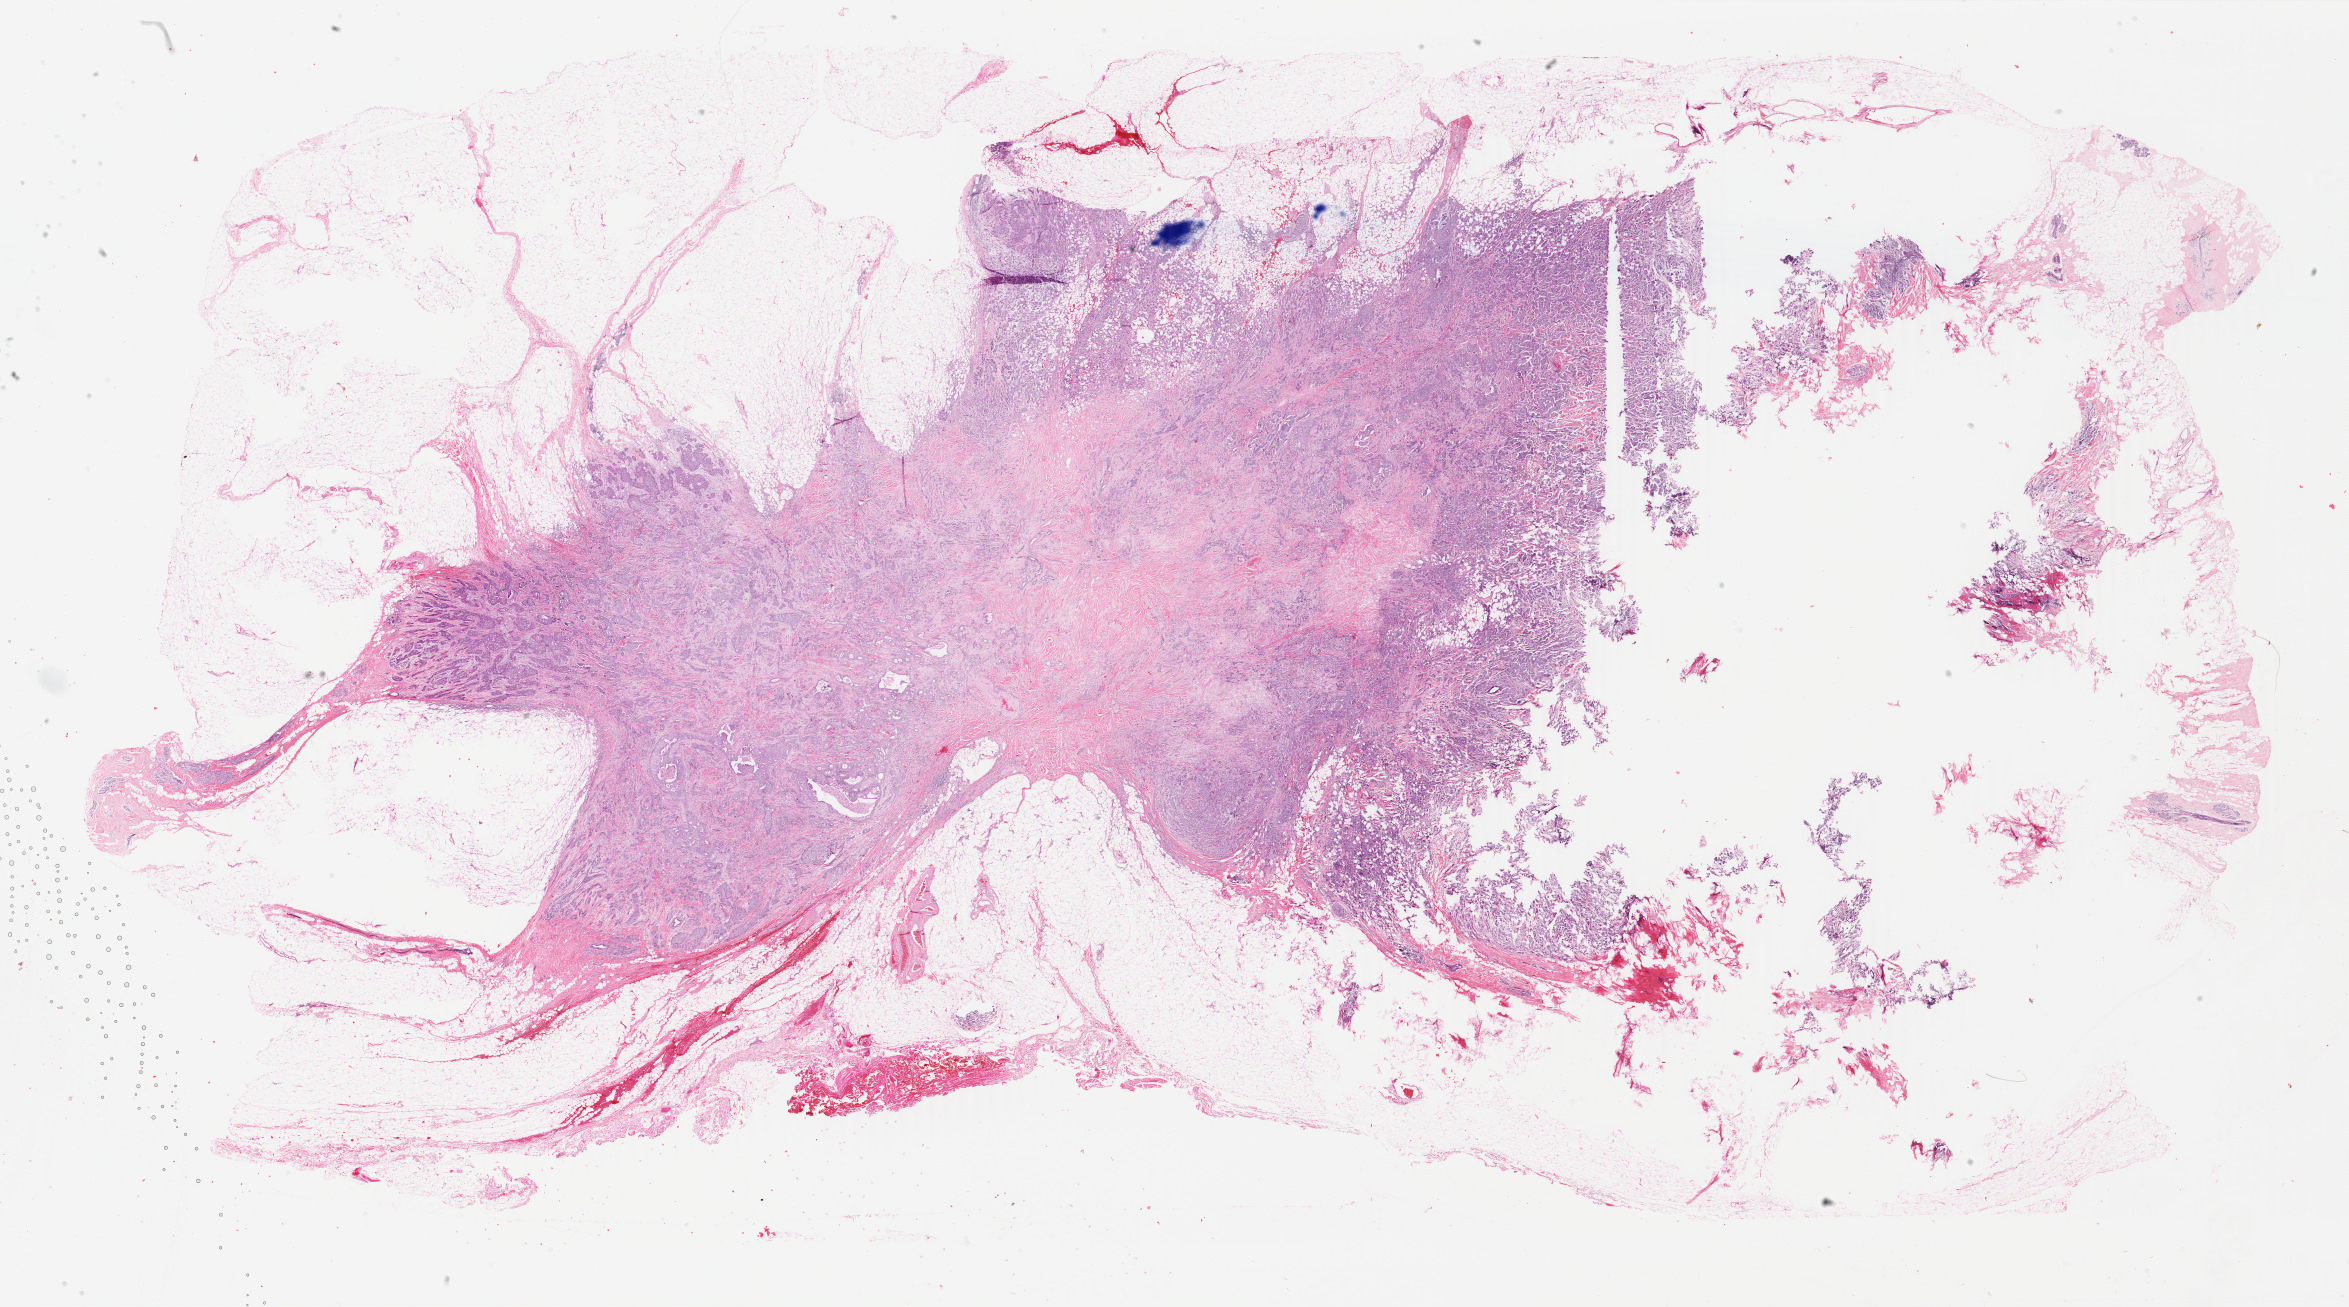
Whole-slide histology image, H&E-stained, shown as a low-resolution overview of the whole scanned area (about 37.4 x 20.8 mm, from a 40x scan). Formalin-fixed paraffin-embedded (FFPE) diagnostic section. Primary tumour sample from the breast. Female patient; age at initial diagnosis 44 years.
Pathologic diagnosis: Infiltrating duct carcinoma, NOS. AJCC pathologic stage: IIIB.